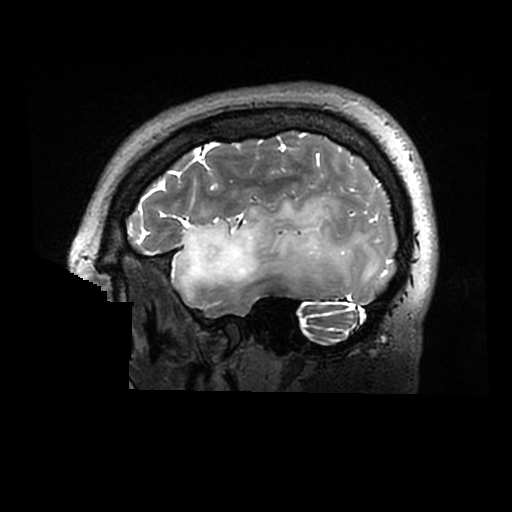
Brain MRI from a brain-tumour surgery series, one sagittal slice. Position 233 of 320 along the scan axis. 0.6 mm slice thickness. 512 × 512 image matrix, field of view 240 × 240 mm. Case-level facts recorded for this patient, not image findings: histopathology: Astrocytoma; WHO grade: 2; IDH mutation: yes.
Outlined on this slice (expert manual segmentation):
- tumour: bounding box <172,197,379,298> (left, top, right, bottom; pixels)